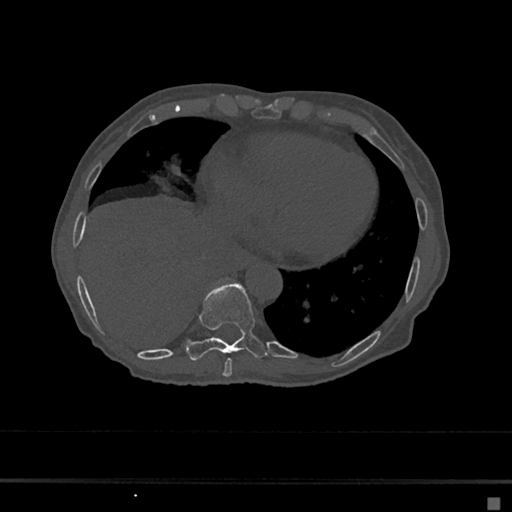
CT including the spine, one axial slice. Slice 276 of 797 in the series (ordered by position). Reconstruction kernel Br40s/3. Bone window (W 1800 / L 400 HU). 0.5 mm slice thickness. 512 × 512 image matrix. Patient: female, 68 years. Case-level facts recorded for this patient, not image findings: primary cancer: renal.
Annotated regions visible in this slice (semi-automatically segmented with operator editing):
- T8 vertebra: box from (x=223, y=358) to (x=232, y=377) px
- T9 vertebra: (x=186, y=283)–(x=268, y=361)